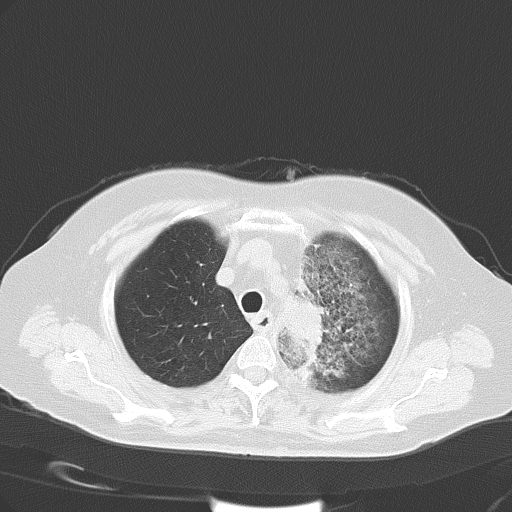
Chest CT, one axial slice; position 44 of 54 along the scan axis; 120 kVp; lung window (W 1500 / L -600 HU); 5 mm slice thickness; 512 × 512 image matrix, field of view 353 × 353 mm. Female patient, age 65 years. From the clinical record (not read from this slice): clinical TNM (as recorded): T2b N1 M0.
Structures marked on this image (rectangle marked by the reading radiologist):
- lung tumour (recorded histology: adenocarcinoma): box from (x=284, y=293) to (x=326, y=356) px